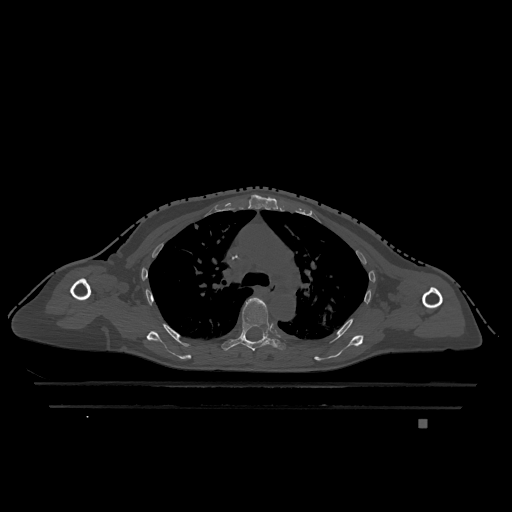
CT including the spine, one axial slice. Position 842 of 1317 along the scan axis. Bone window (W 1800 / L 400 HU). 0.5 mm slice thickness. 512 × 512 image matrix, field of view 500 × 500 mm. Female patient, age 74 years. From the clinical record (not read from this slice): primary cancer: lung; vertebrae with lytic lesions (as recorded): T1, T4, T5, T6, L4, L5.
Structures marked on this image (semi-automatic segmentation, software-assisted and operator-edited):
- T5 vertebra: bounding box <222,297,286,351> (left, top, right, bottom; pixels)